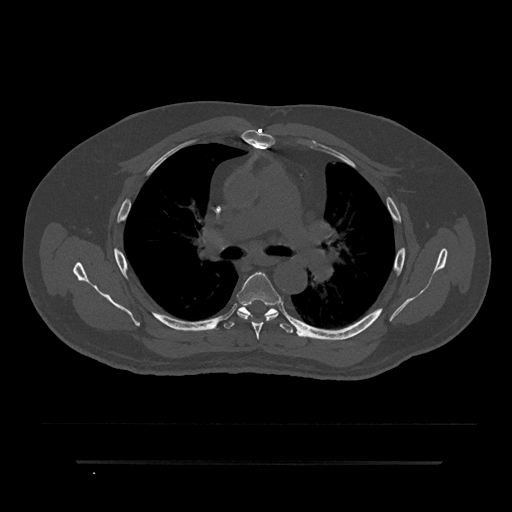
CT including the spine, one axial slice; slice 558 of 797 in the series (ordered by position); 120 kVp; bone window (W 1800 / L 400 HU); 512 × 512 image matrix. Male patient, age 59 years. Case-level facts recorded for this patient, not image findings: primary cancer: bile ducts; vertebrae with lytic lesions (as recorded): T10.
Structures marked on this image (semi-automatic segmentation, software-assisted and operator-edited):
- T5 vertebra: bounding box (x1, y1, x2, y2) in pixels: (237, 272, 279, 340)
- T6 vertebra: (224, 299, 293, 333)